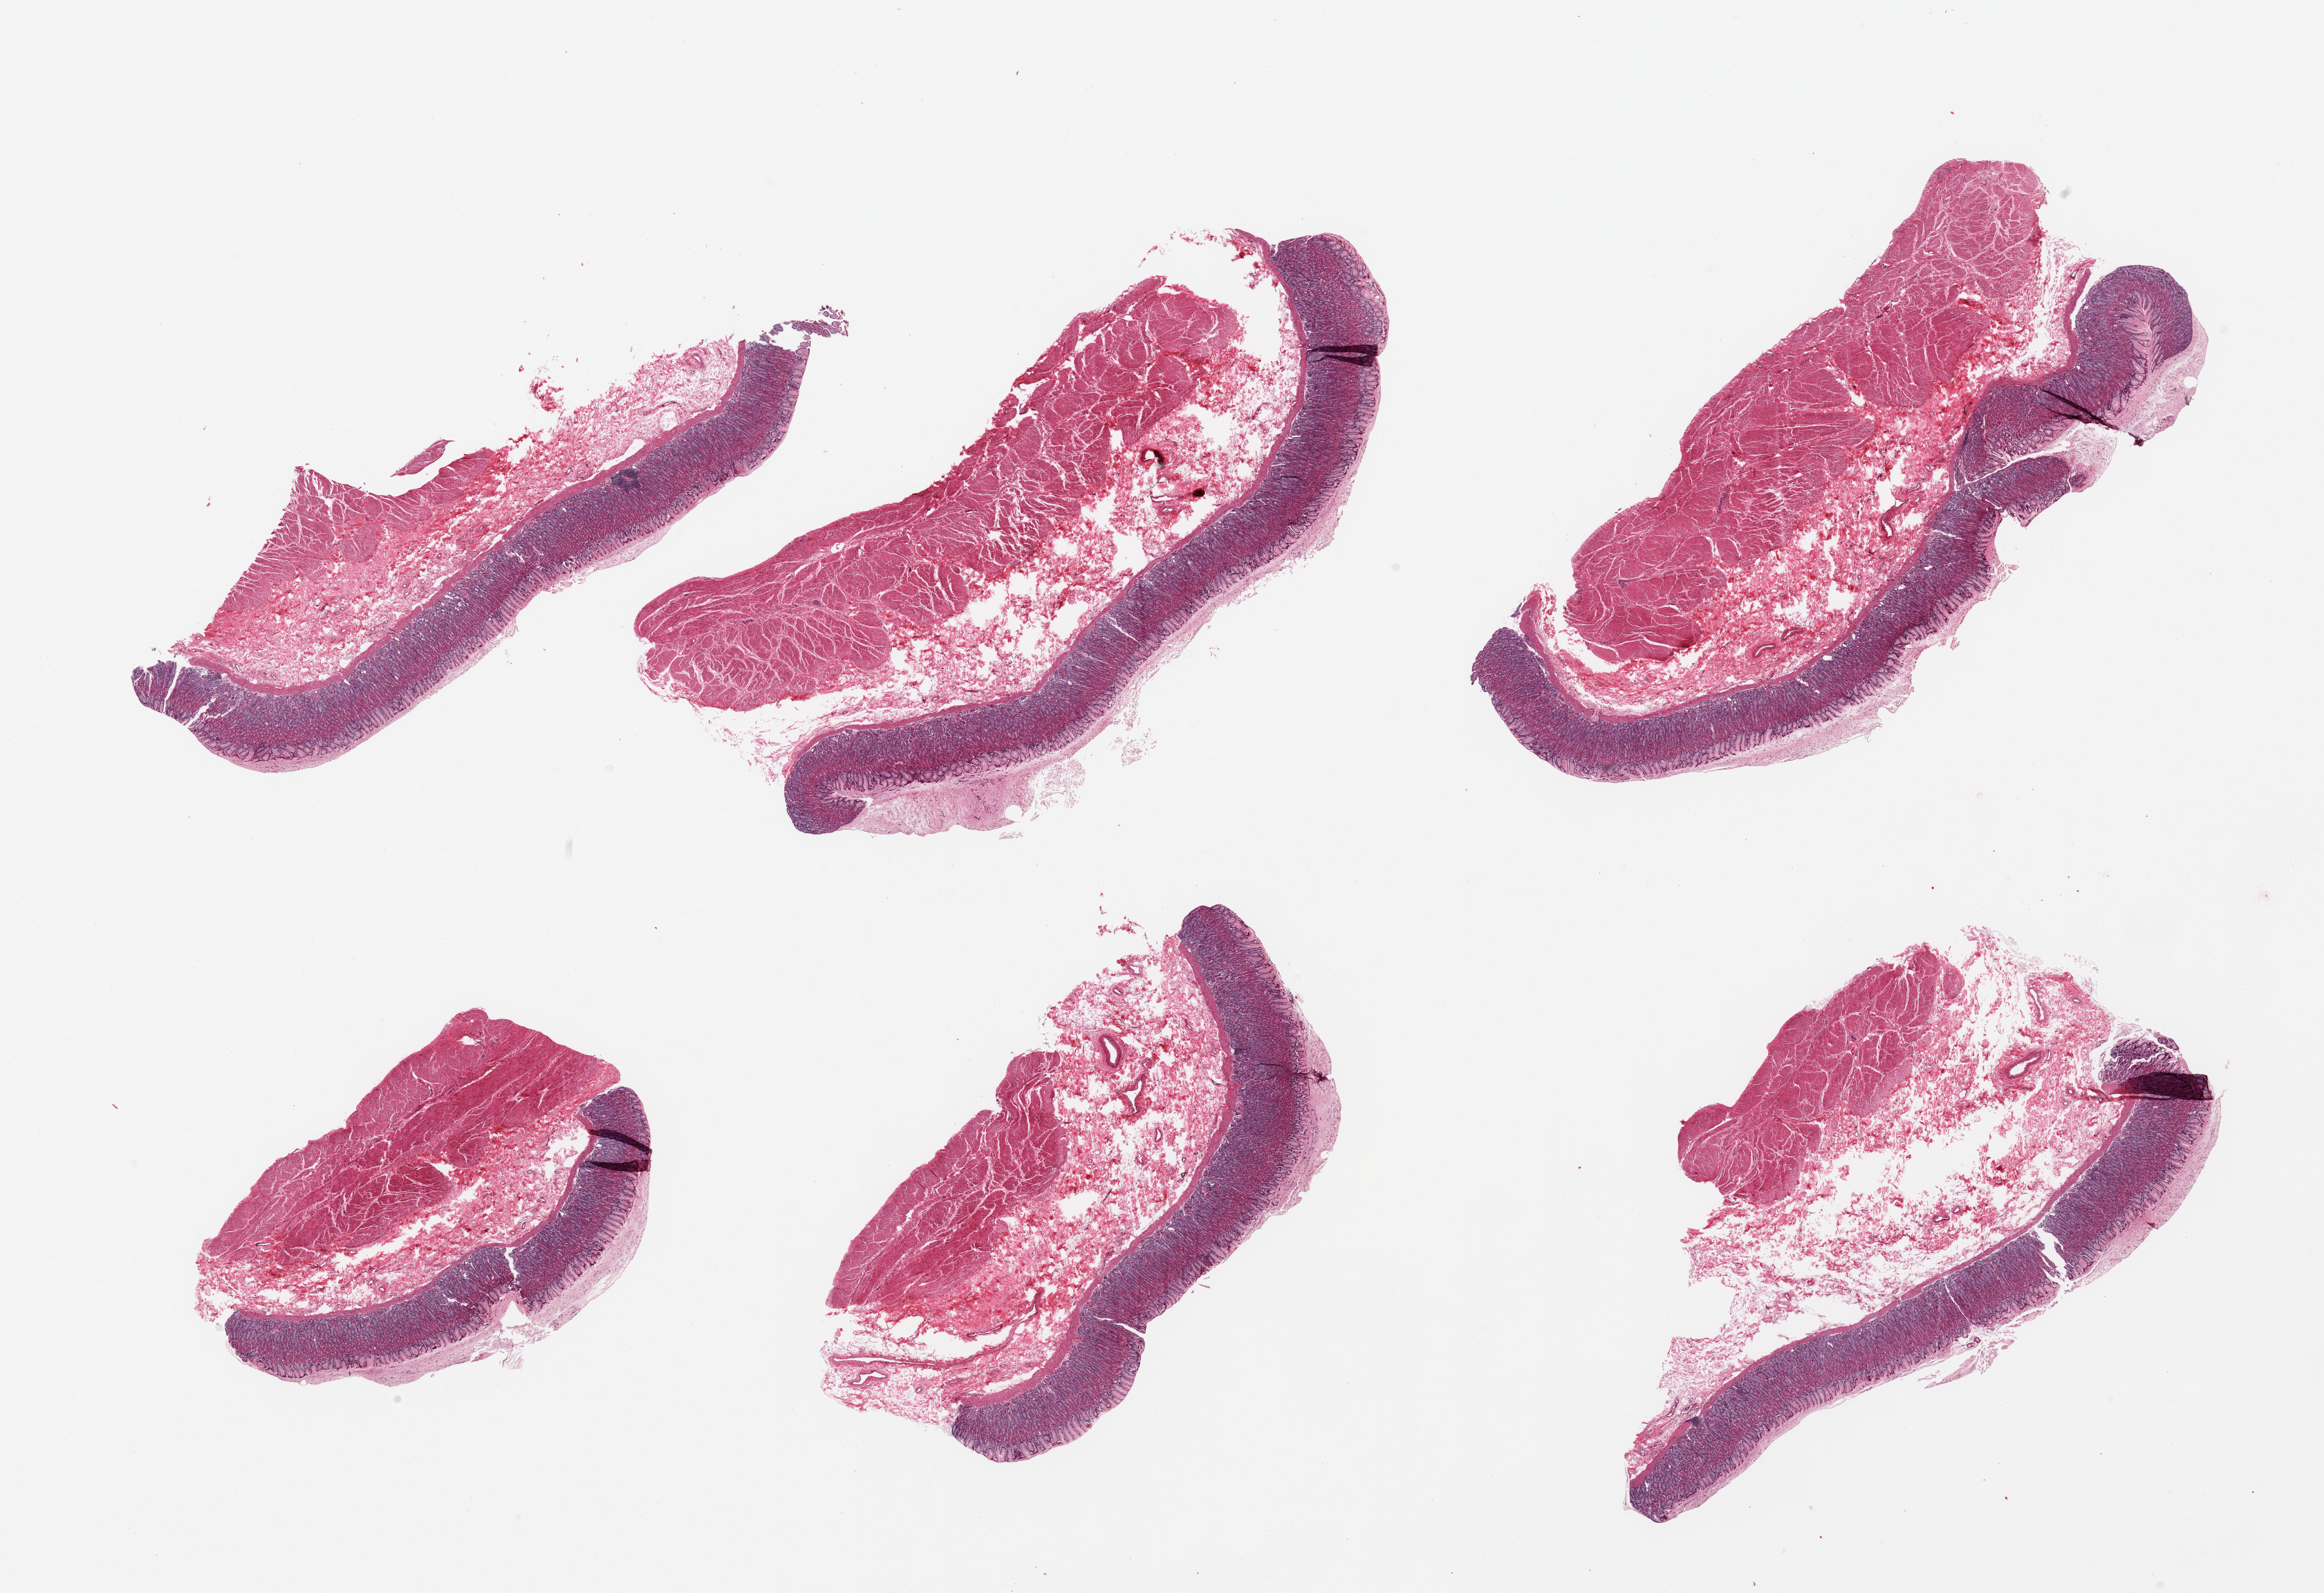
Whole-slide image, H&E stain, low-resolution overview of the scanned area, about 26.6 x 18.2 mm. PAXgene-fixed paraffin-embedded (PFPE) section. Section of stomach (target tissue). Donor tissue sample. Female donor.
- pathologist's review note for this sample: 6 pieces; essentially well preserved gastric mucosa and muscularis